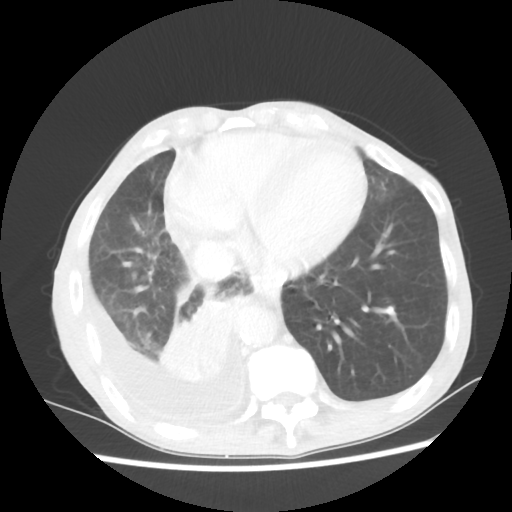
Chest CT, one axial slice; position 18 of 60 along the scan axis; reconstruction kernel STANDARD; 80 kVp; lung window (W 1500 / L -600 HU); 512 × 512 image matrix, field of view 335 × 335 mm. Male patient, age 76 years. Case-level facts recorded for this patient, not image findings: clinical TNM (as recorded): T3 N3 M1a; histopathological grade: G3.
Annotated regions visible in this slice (bounding box drawn by a radiologist):
- lung tumour (recorded histology: squamous cell carcinoma): box from (x=155, y=289) to (x=240, y=386) px